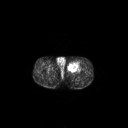
FDG PET of an extremity soft-tissue mass (from a PET/CT study), one axial slice; position 262 of 267 along the scan axis; 128 × 128 image matrix. Patient: male, 63 years. Case-level facts recorded for this patient, not image findings: histological type: pleiomorphic liposarcoma; grade: high; site of the primary tumour: left thigh.
Structures marked on this image (expert contour drawn on MRI and transferred to this co-registered scan by the dataset authors):
- gross tumour volume including surrounding oedema: bounding box <68,61,80,71> (left, top, right, bottom; pixels)
- gross tumour volume (mass): <68,63,77,70>